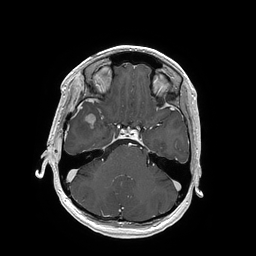
Brain MRI from a brain-tumour surgery series, one axial slice; T1-weighted post-contrast; 1 mm slice thickness; 256 × 256 image matrix. Case-level facts recorded for this patient, not image findings: histopathology: Glioblastoma; WHO grade: 4; IDH mutation: no; tumour location: Right Insular.
Outlined on this slice (manually delineated by an expert):
- tumour: box from (x=85, y=114) to (x=96, y=128) px